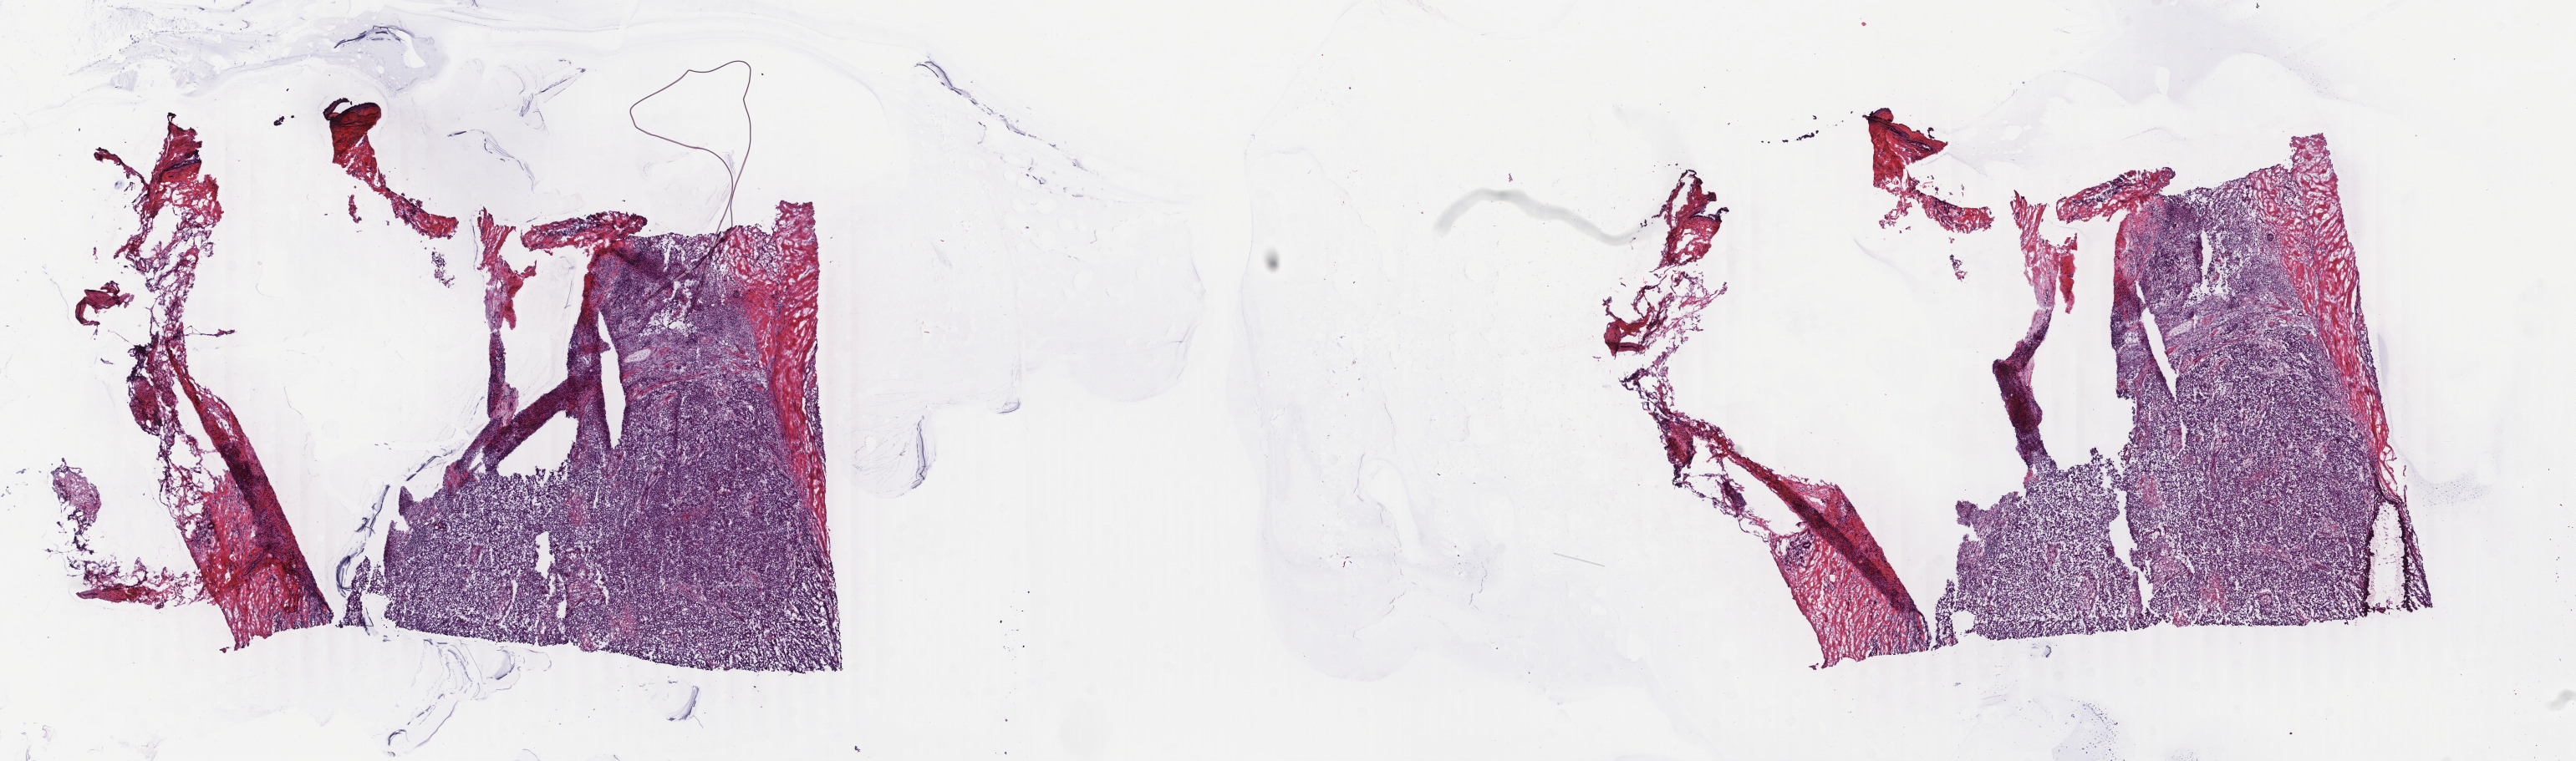
Whole-slide histology image, H&E — low-resolution overview of the scanned area, about 24.5 x 7.2 mm (acquisition: 40x scan). Frozen section from the top of the tissue portion. Sample: primary tumour, breast. Female, age 62 years at initial diagnosis. Pathologist review of this section (percent, as recorded): tumour cells 70%, tumour nuclei 70%, normal cells 0%, stromal cells 15%, necrosis 15%. Infiltration values recorded for this section: lymphocyte infiltration 40%, monocyte infiltration 20%, neutrophil infiltration 20%.
• laterality: left
• AJCC pathologic stage: IIA
• diagnosis: Lobular carcinoma, NOS